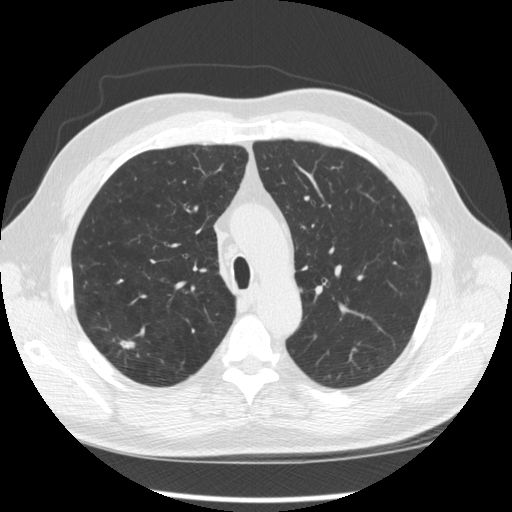
Low-dose screening chest CT, axial slice, second annual screen, lung window (W 1500 / L -600 HU), standard (soft-tissue) reconstruction kernel (STANDARD), slice 82 of 289 in the series. Male, age 64 years at enrolment. Former smoker at enrolment.
• Expert-annotated lung lesion, bounding box <104,327,150,368> (left, top, right, bottom; pixels).
• The screening reader recorded 3 non-calcified nodules or masses ≥4 mm on this exam (right upper lobe, right upper lobe, right upper lobe); which of them this box marks is not recorded.
• Lung cancer was diagnosed 411 days after this screen (after the third annual screen): adenocarcinoma, NOS, right upper lobe, moderately differentiated (G2), stage IA (AJCC 6th edition), 14 mm at pathology.